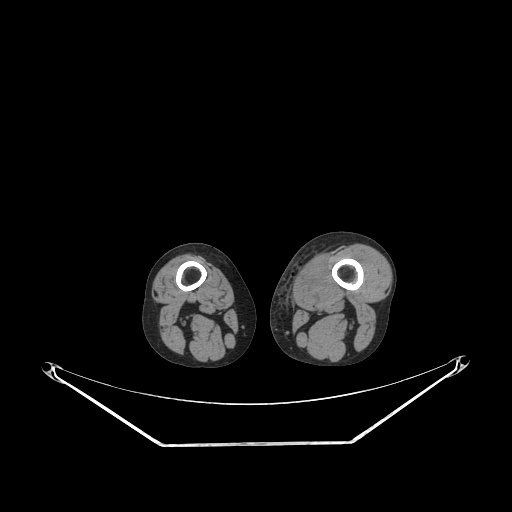
CT of an extremity soft-tissue mass (from a PET/CT study), one axial slice. Slice 205 of 267 in the series (ordered by position). Reconstruction kernel STANDARD. 140 kVp. Soft-tissue window (W 400 / L 40 HU). 512 × 512 image matrix, field of view 500 × 500 mm. Male patient. Case-level facts recorded for this patient, not image findings: histological type: pleiomorphic leiomyosarcoma; grade: high; site of the primary tumour: left thigh.
Outlined on this slice (expert contour drawn on MRI and transferred to this co-registered scan by the dataset authors):
- gross tumour volume including surrounding oedema: bounding box <304,256,327,286> (left, top, right, bottom; pixels)